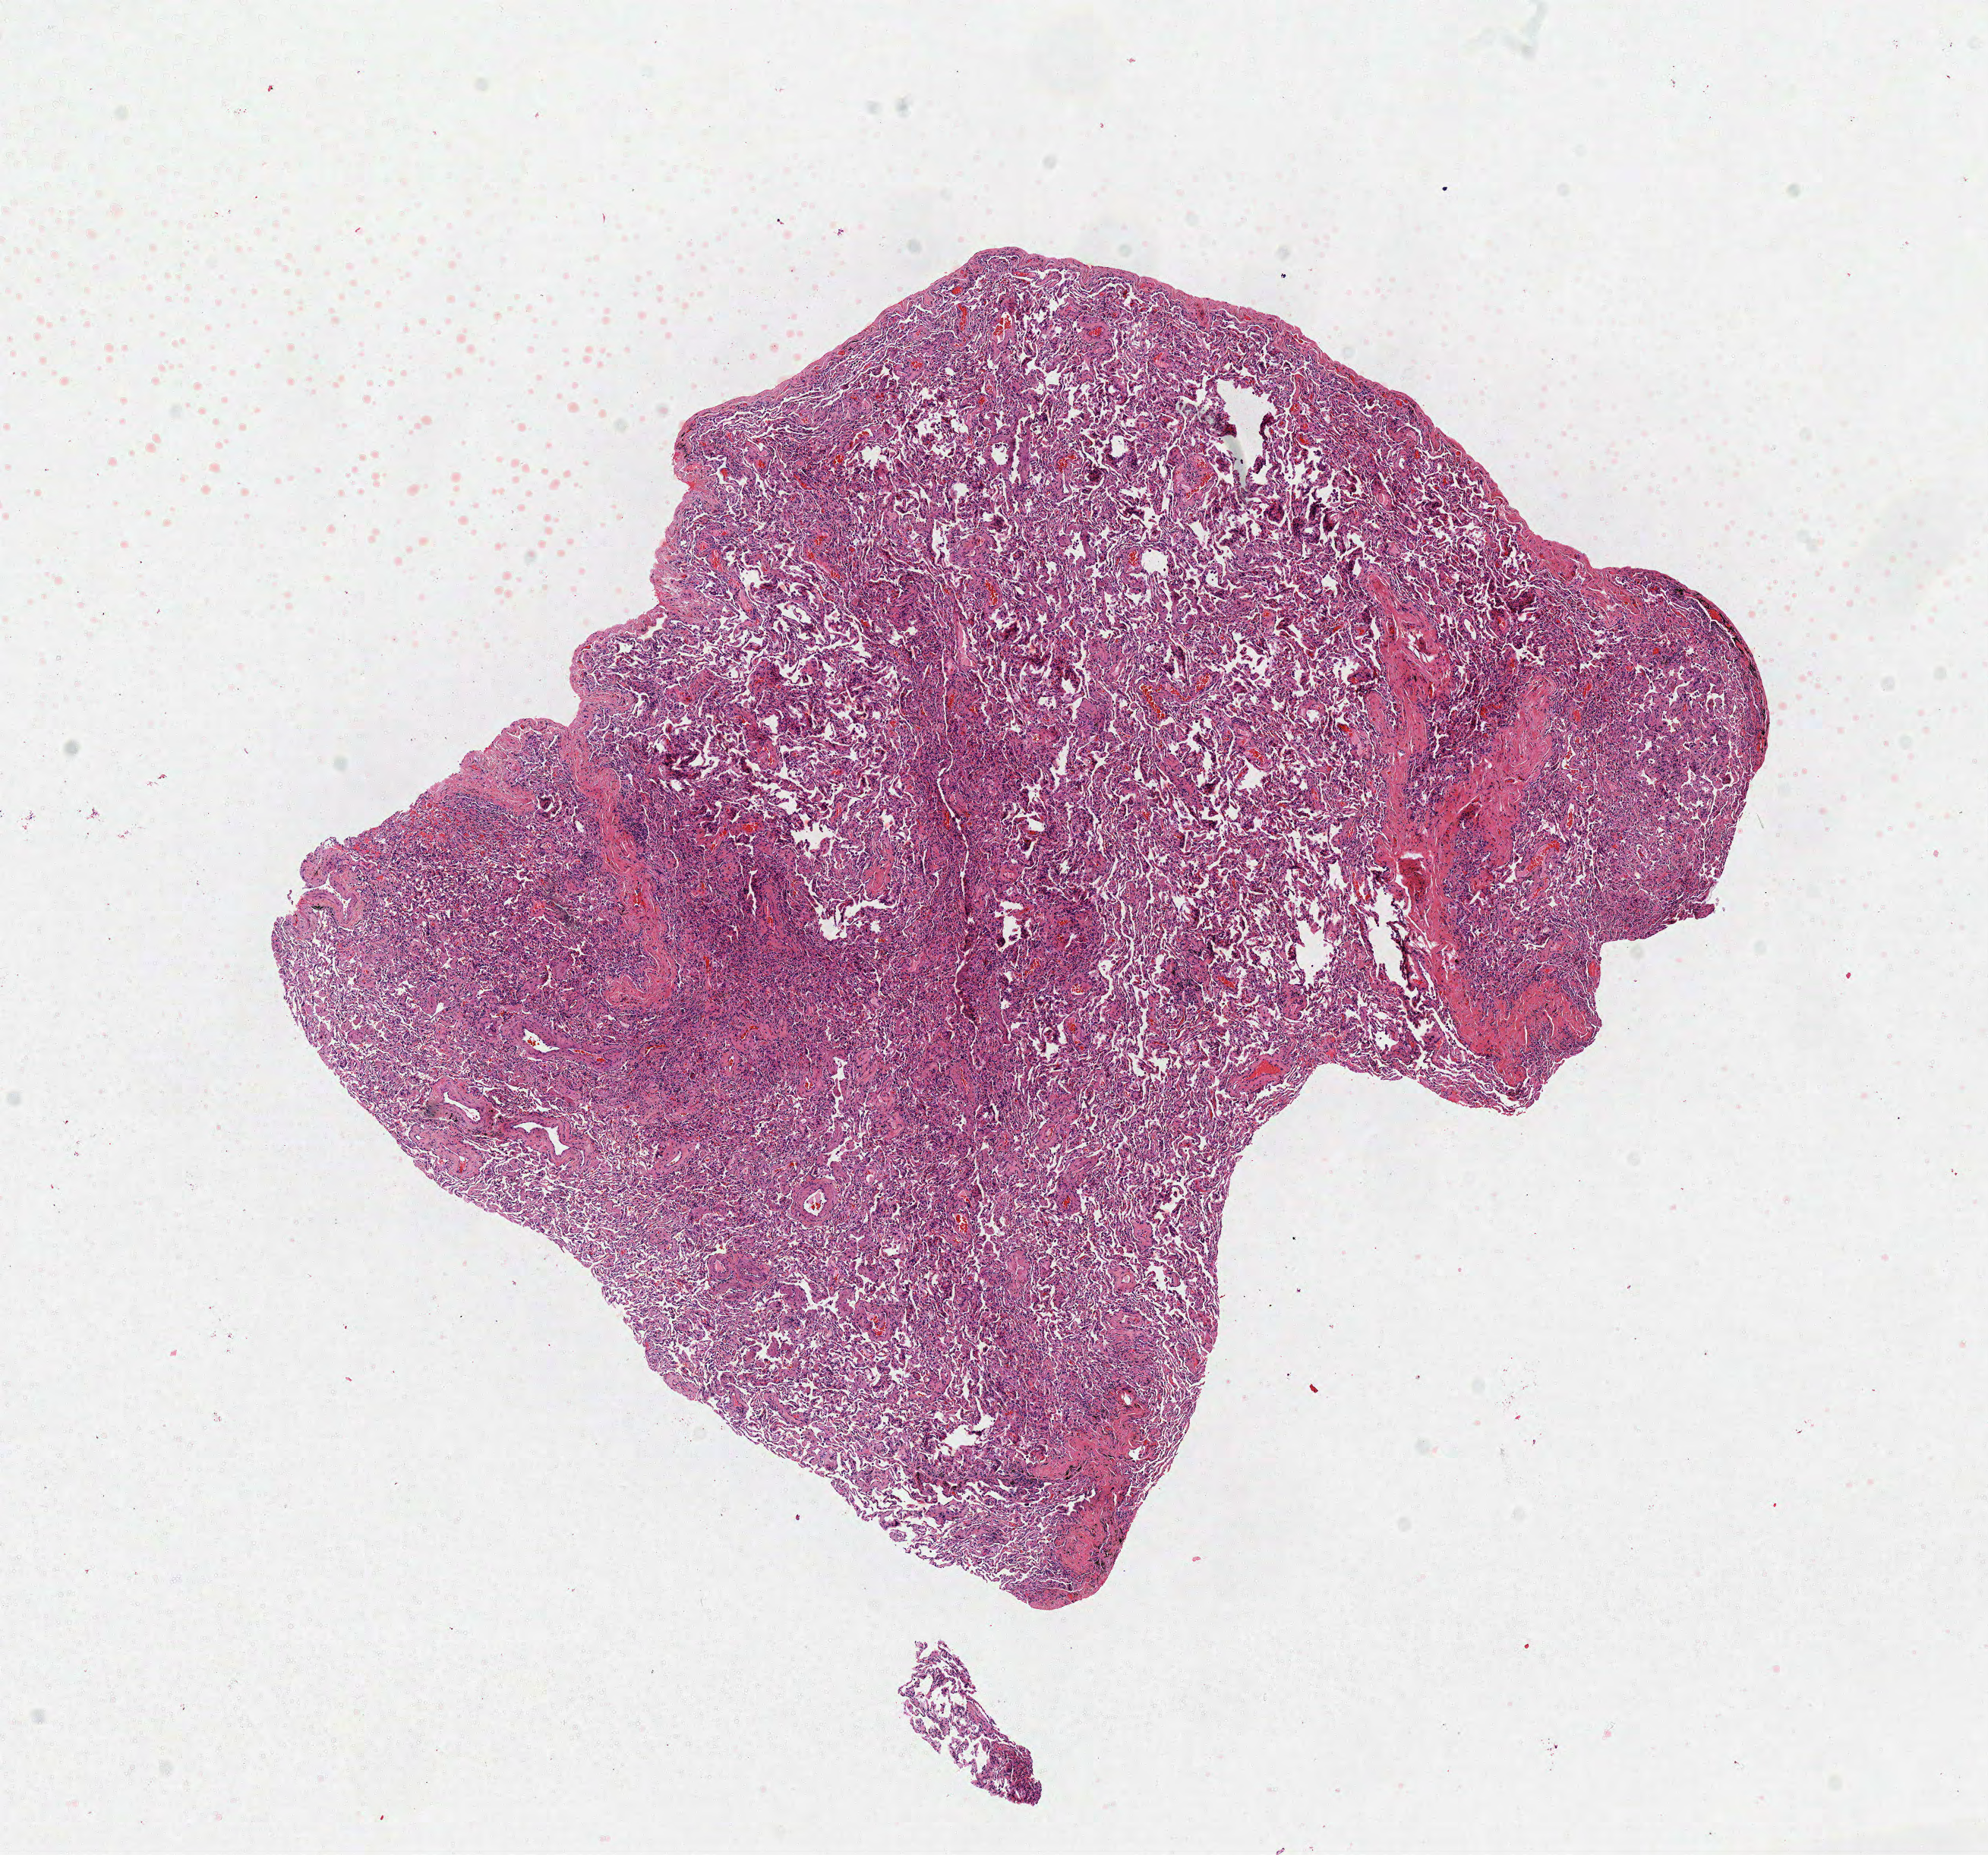
Whole-slide histology image, H&E — low-resolution overview of the scanned area, about 10.3 x 9.6 mm. Frozen section from the top of the tissue portion. Solid tissue normal (non-tumour tissue) sample from the lung. Female patient; age at initial diagnosis 62 years.
This section: solid tissue normal sample (biorepository sample class). Patient diagnosis: Adenocarcinoma, NOS (lower lobe, lung).